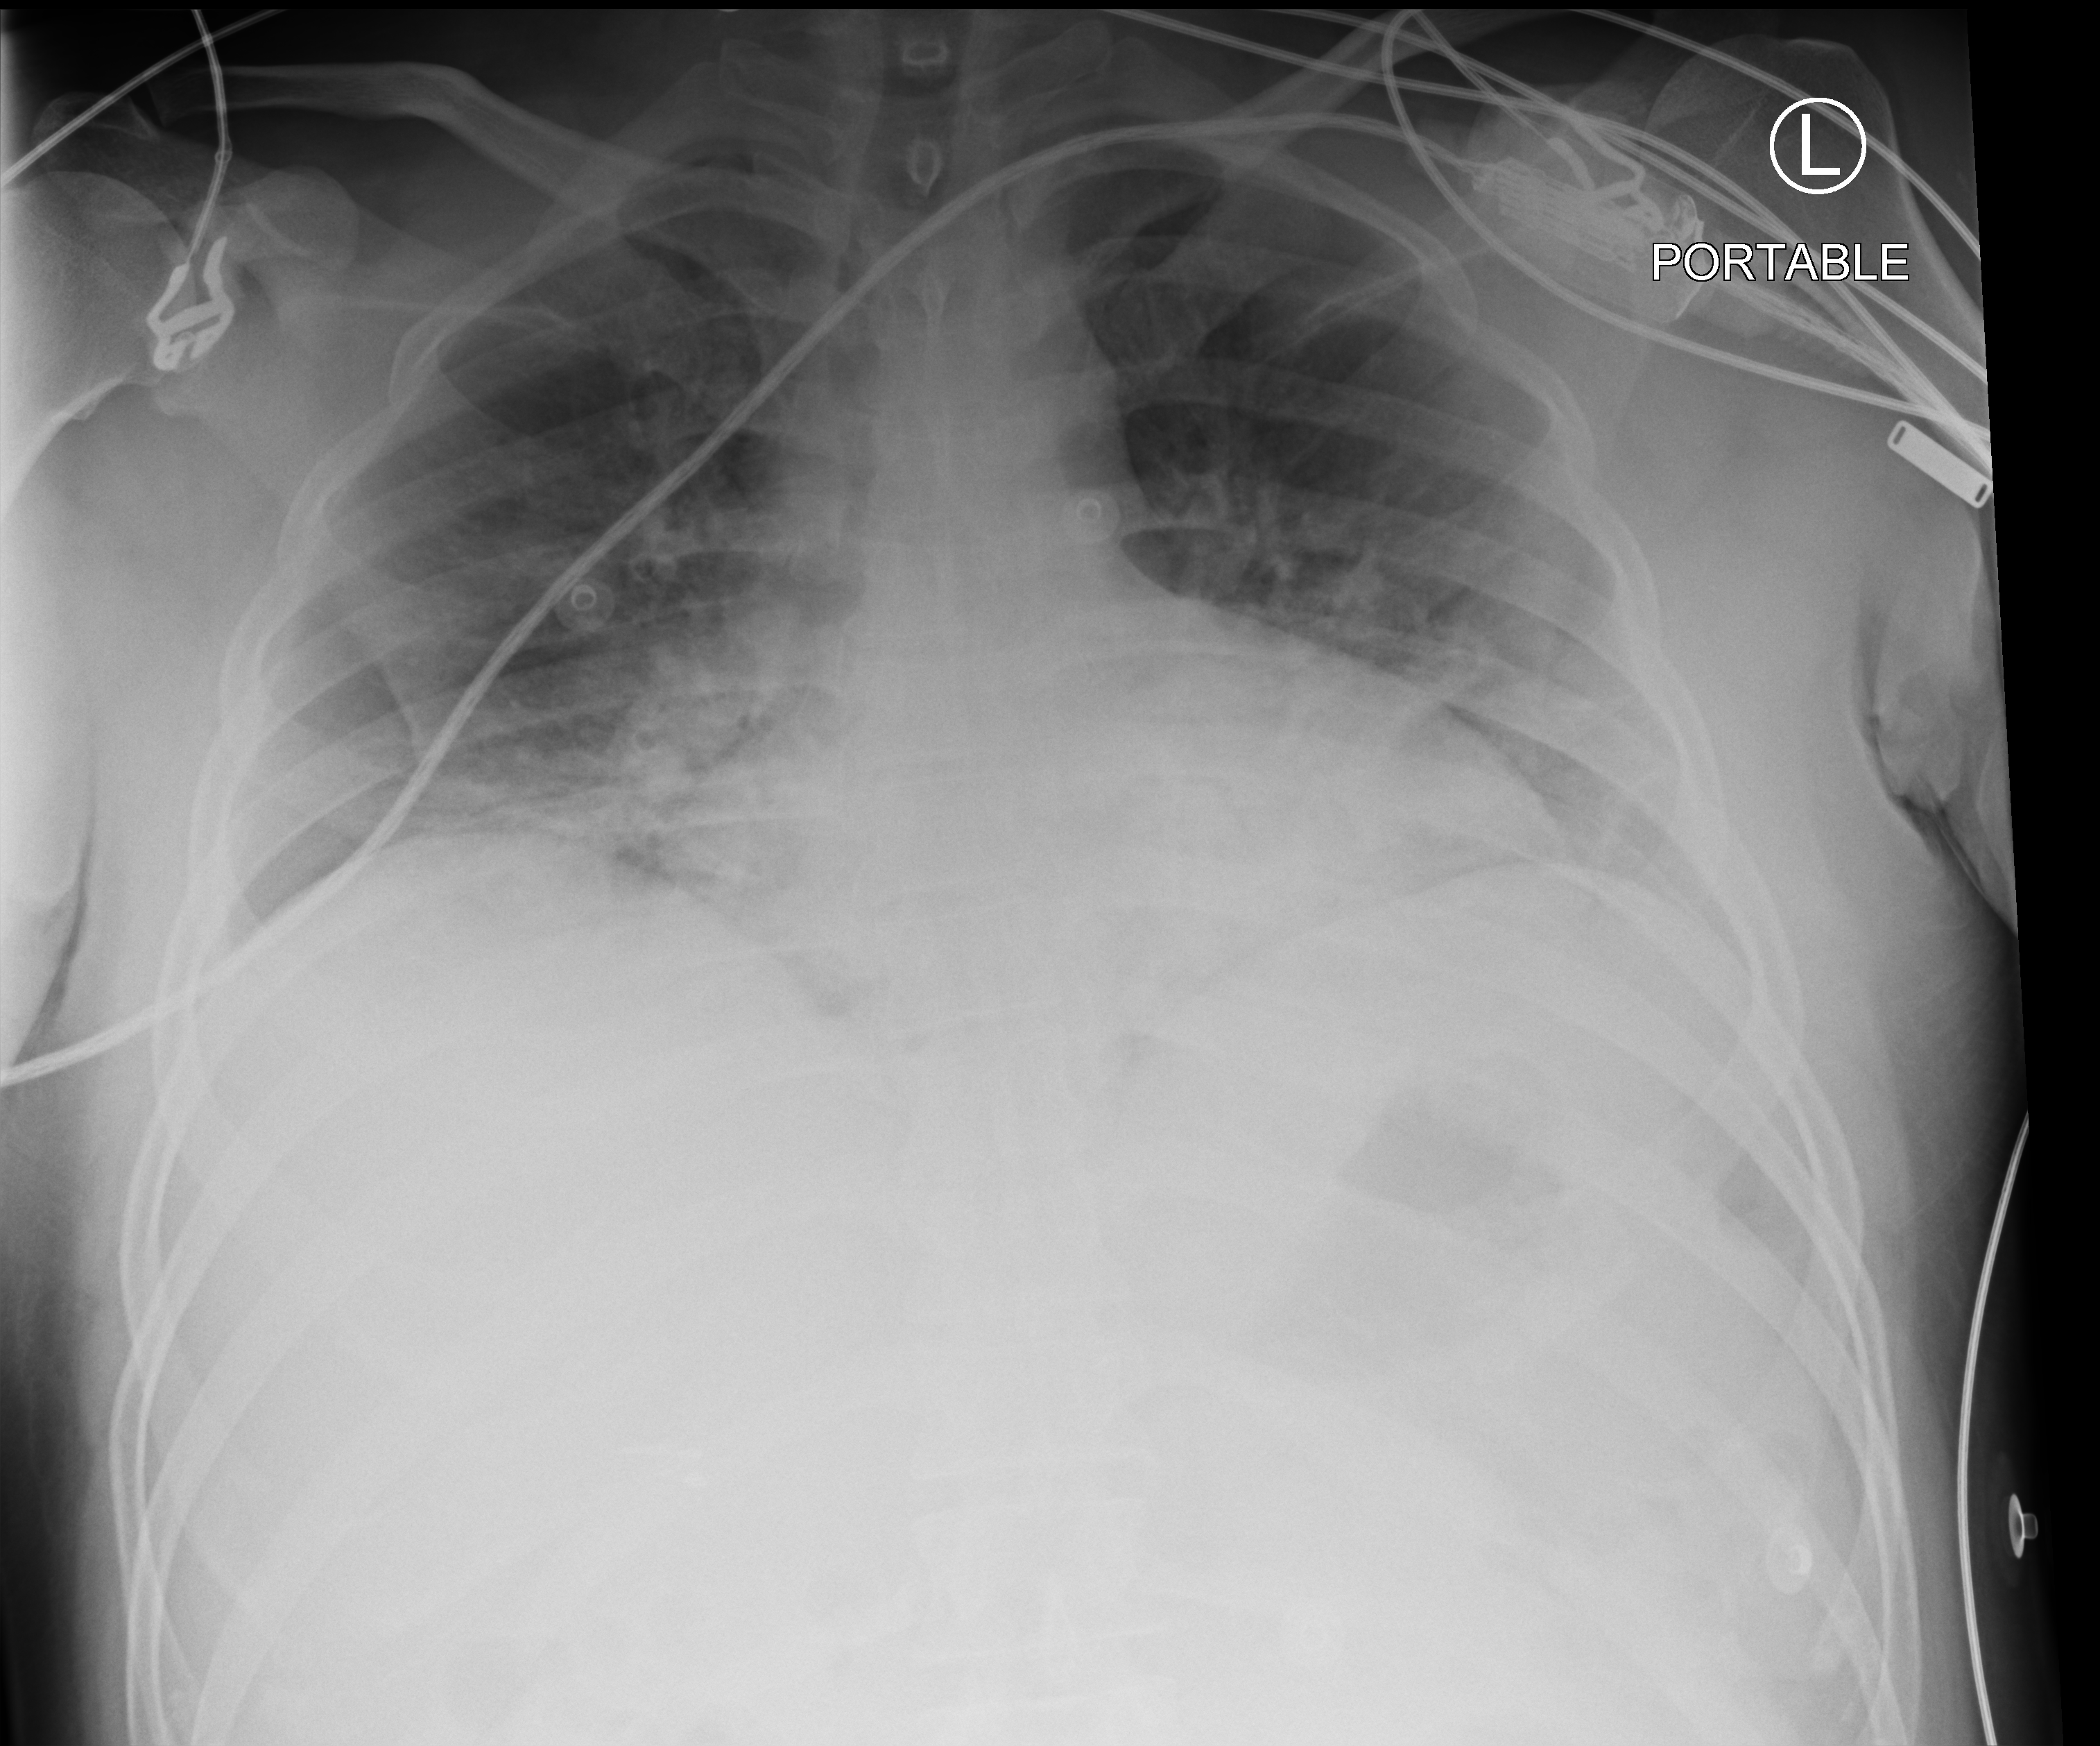
Bedside chest radiograph (computed radiography); anteroposterior (AP) projection. Male patient hospitalised with COVID-19, age 18–59 years.
Admission-level facts for this patient (not findings on this image; timing relative to this image not recorded):
- other chronic lung disease (admission record): no